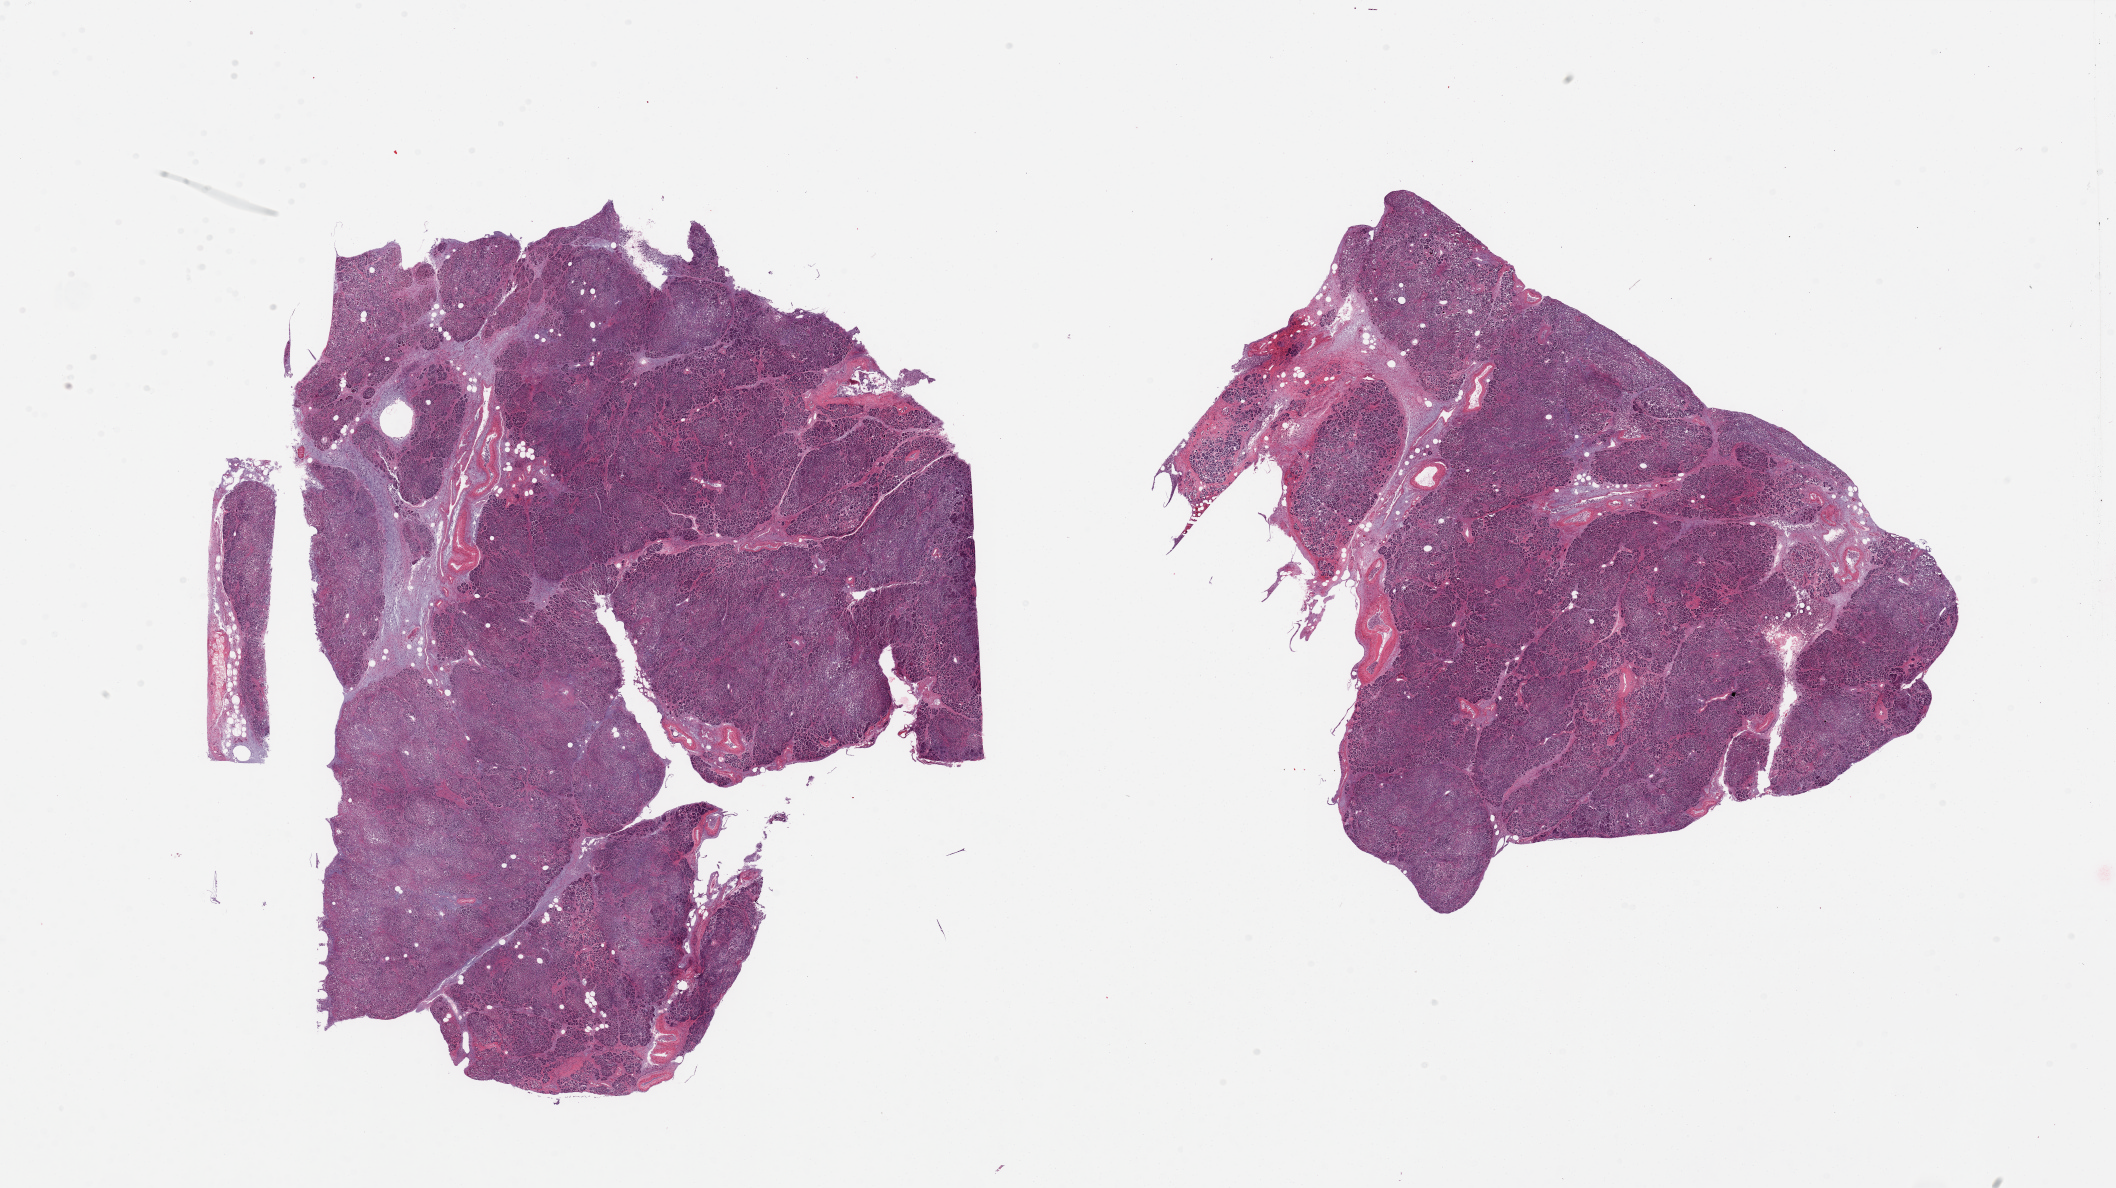
Whole-slide image, haematoxylin and eosin stain, shown as a low-resolution overview of the whole scanned area (about 33.5 x 18.8 mm, acquisition: 20x scan); PAXgene-fixed paraffin-embedded (PFPE) section; target tissue: pancreas; tissue donor sample.
Pathologist's review note for this sample: 2 pieces, advanced autolysis/saponification. Islets not well visualized.